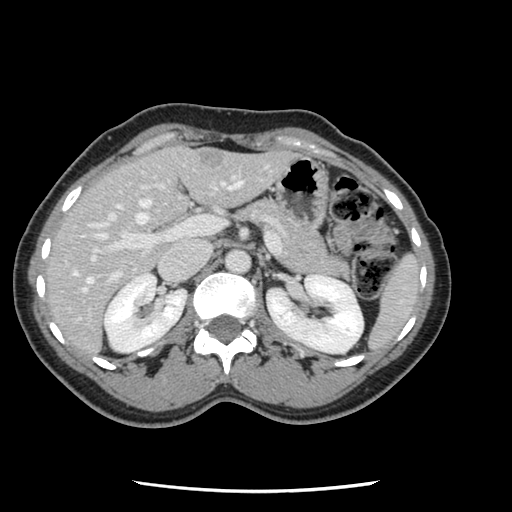
Contrast-enhanced abdominal CT, one axial slice. Slice 67 of 134 in the series (ordered by position). 120 kVp. Intravenous contrast given. Soft-tissue window (W 400 / L 40 HU). 2.5 mm slice thickness. 512 × 512 image matrix. Female patient, age 43 years. From the clinical record (not read from this slice): diagnosis: colorectal cancer liver metastases, imaged before liver resection; multiple liver metastases: yes; largest metastasis: 3.4 cm; disease in both lobes: yes.
Structures marked on this image (outlined manually by an expert reader):
- hepatic veins: bounding box [x1, y1, x2, y2] px = [73, 182, 241, 293]
- liver: [46, 147, 293, 353]
- planned liver remnant (the part of the liver to remain after resection): [46, 150, 186, 304]
- portal vein (with intrahepatic branches): [87, 176, 269, 320]
- liver metastasis: [198, 154, 224, 168]